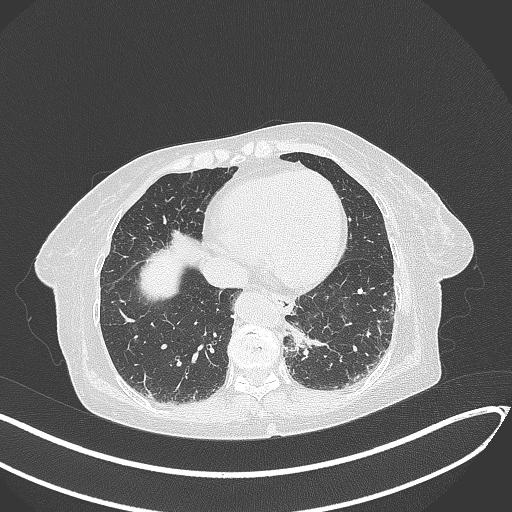
Chest CT, one axial slice; position 57 of 324 along the scan axis; reconstruction kernel B70f; 120 kVp; lung window (W 1500 / L -600 HU); 1 mm slice thickness; 512 × 512 image matrix, field of view 400 × 400 mm. Patient: female, 82 years. From the clinical record (not read from this slice): clinical TNM (as recorded): T1b N0 M1.
Structures marked on this image (rectangle marked by the reading radiologist):
- lung tumour (recorded histology: adenocarcinoma): bounding box (x1, y1, x2, y2) in pixels: (280, 321, 337, 363)